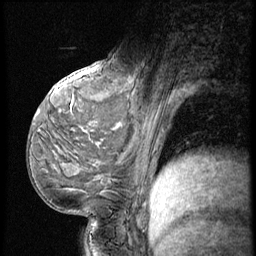
Breast MRI (dynamic contrast-enhanced), one sagittal slice; slice 35 of 56 in the series (ordered by position); 3 images stored at this slice position (order not interpretable as contrast timing); 1.5 T; TE 4.2 ms, TR 9 ms; 2.5 mm slice thickness; 256 × 256 image matrix, field of view 180 × 180 mm. Patient: female, 54 years. Case-level facts recorded for this patient, not image findings: setting: breast cancer imaged before/during neoadjuvant chemotherapy; receptor status: triple-negative.
Annotated regions visible in this slice (semi-automatic segmentation, software-assisted and operator-edited):
- analysis volume of interest (the breast-tissue region the enhancement analysis was run in; not a lesion): bounding box <99,53,149,102> (left, top, right, bottom; pixels)
- tumour enhancement mask (voxels above the 140 % enhancement threshold inside the analysis volume of interest): <132,76,138,82>